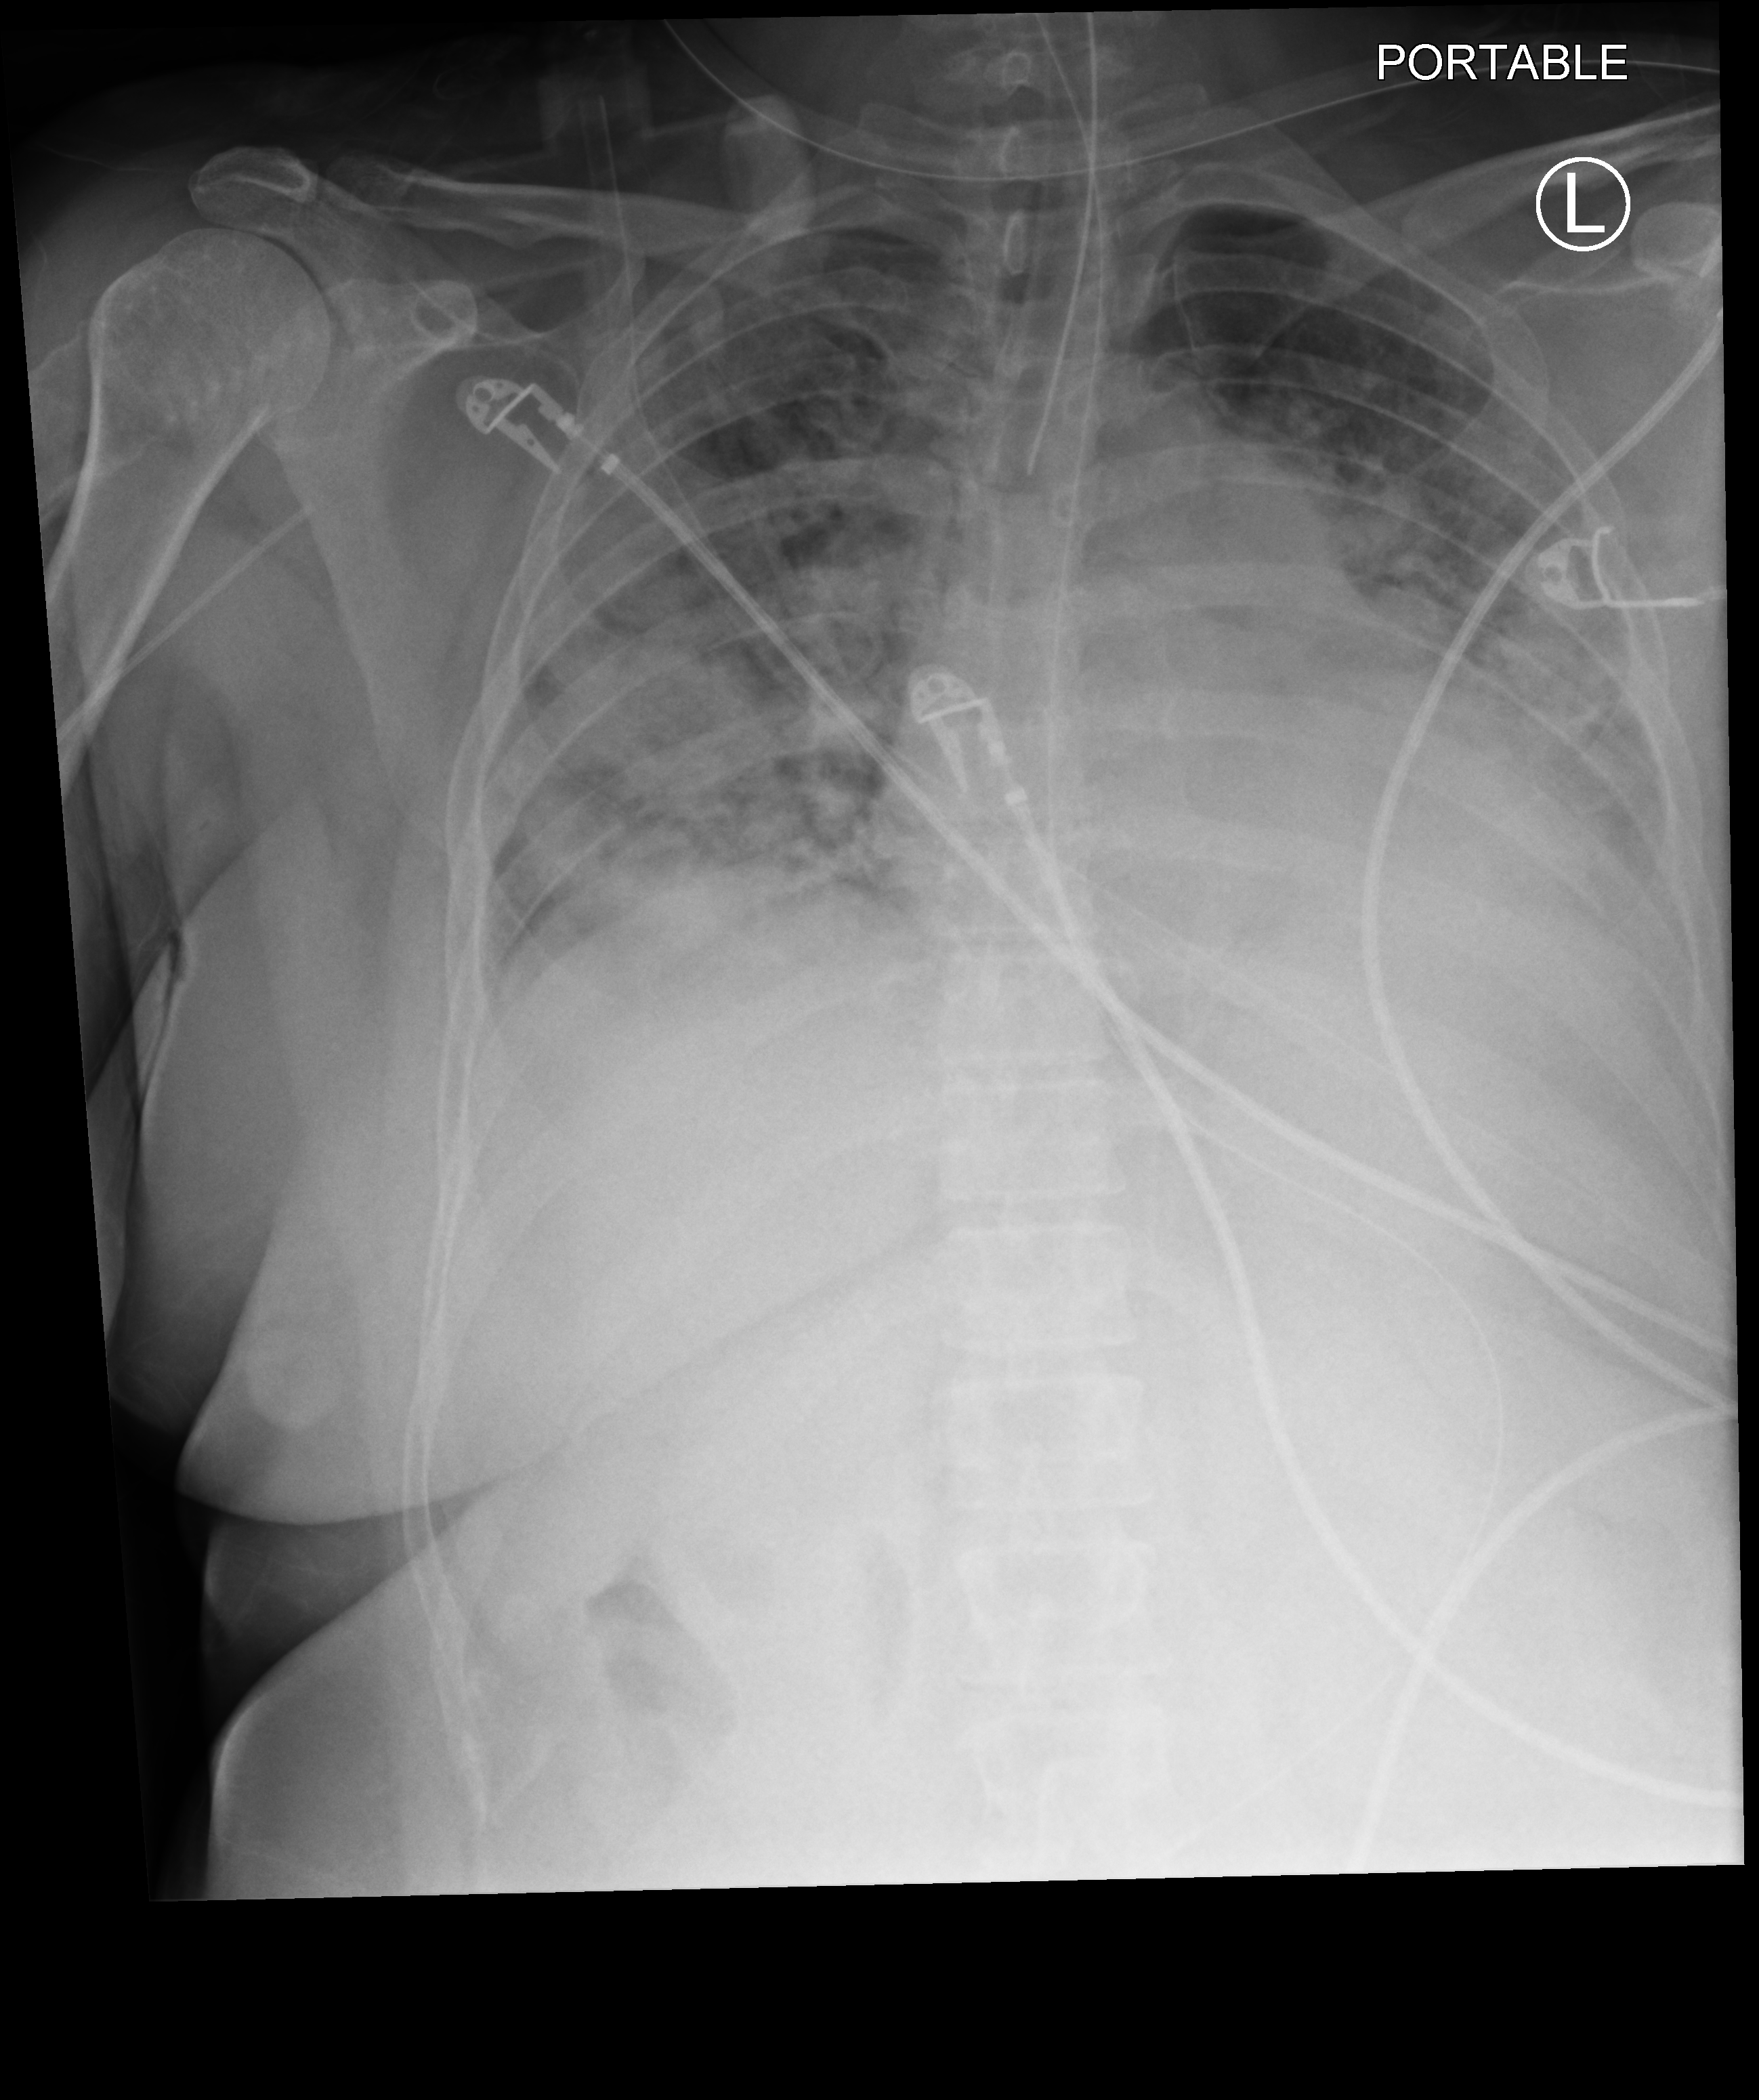
Chest X-ray (portable). Female patient hospitalised with COVID-19, age 18–59 years.
Hospital-stay facts (about this admission, not read from this image; timing relative to this image not recorded): diabetes (admission record): yes; COPD (admission record): no; chronic kidney disease (admission record): no.